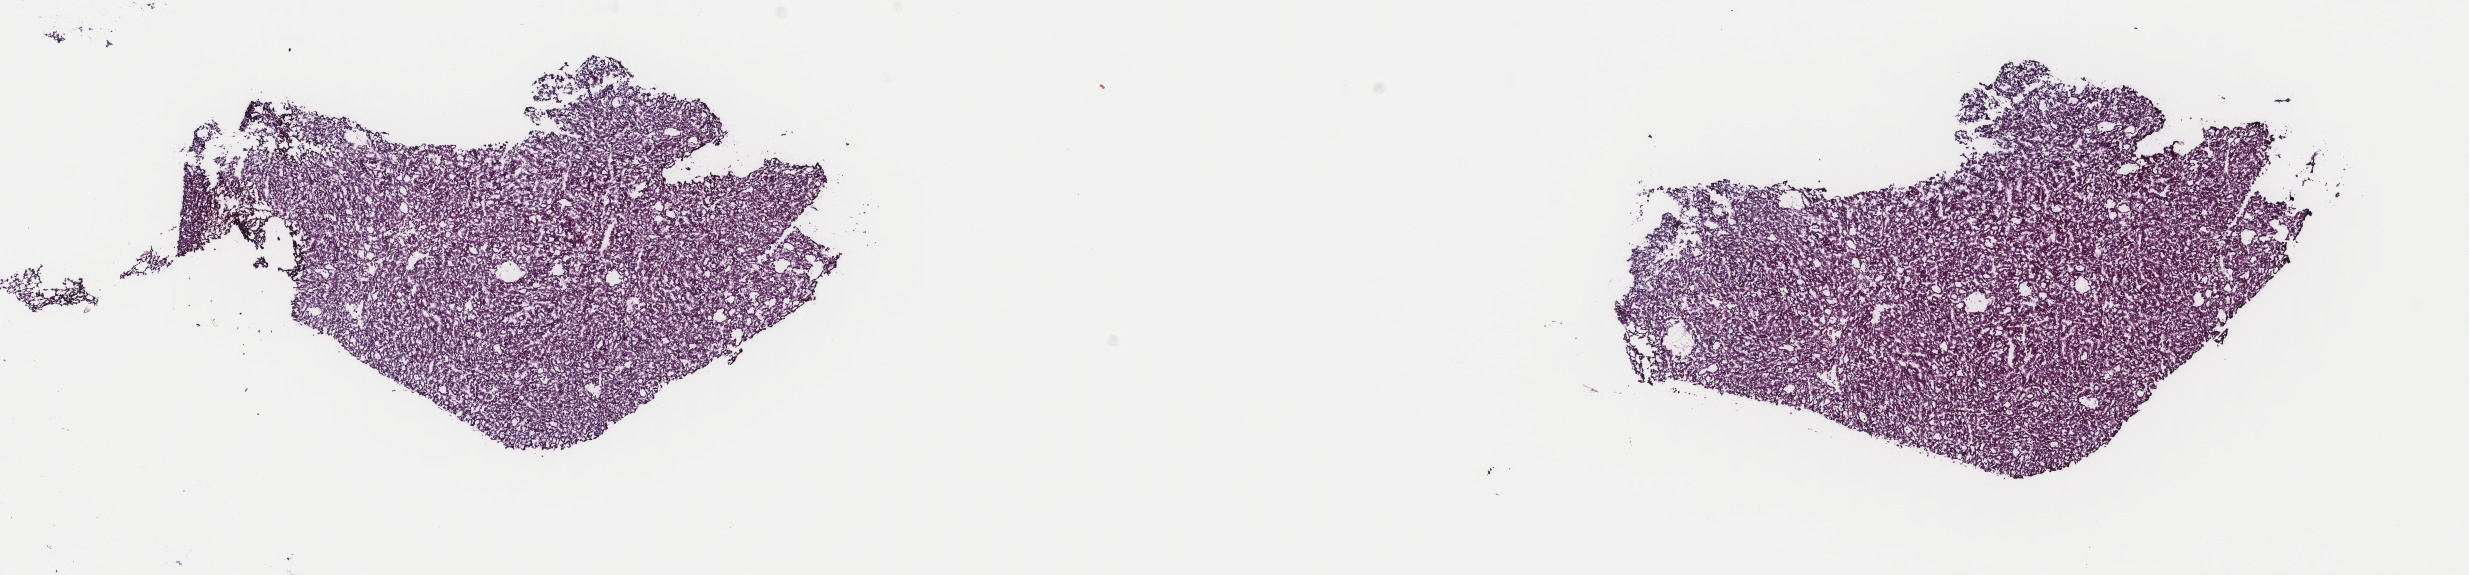
Digitized H&E-stained tissue section (whole slide), a low-resolution overview of the entire scanned area, about 19.6 x 4.6 mm (from a 40x scan), frozen section from the top of the tissue portion, sample: primary tumour, liver. Male, age 65 years at initial diagnosis. Composition of this section per pathologist review: tumour cells 100%, tumour nuclei 80%.
Diagnosis: Hepatocellular carcinoma, NOS.